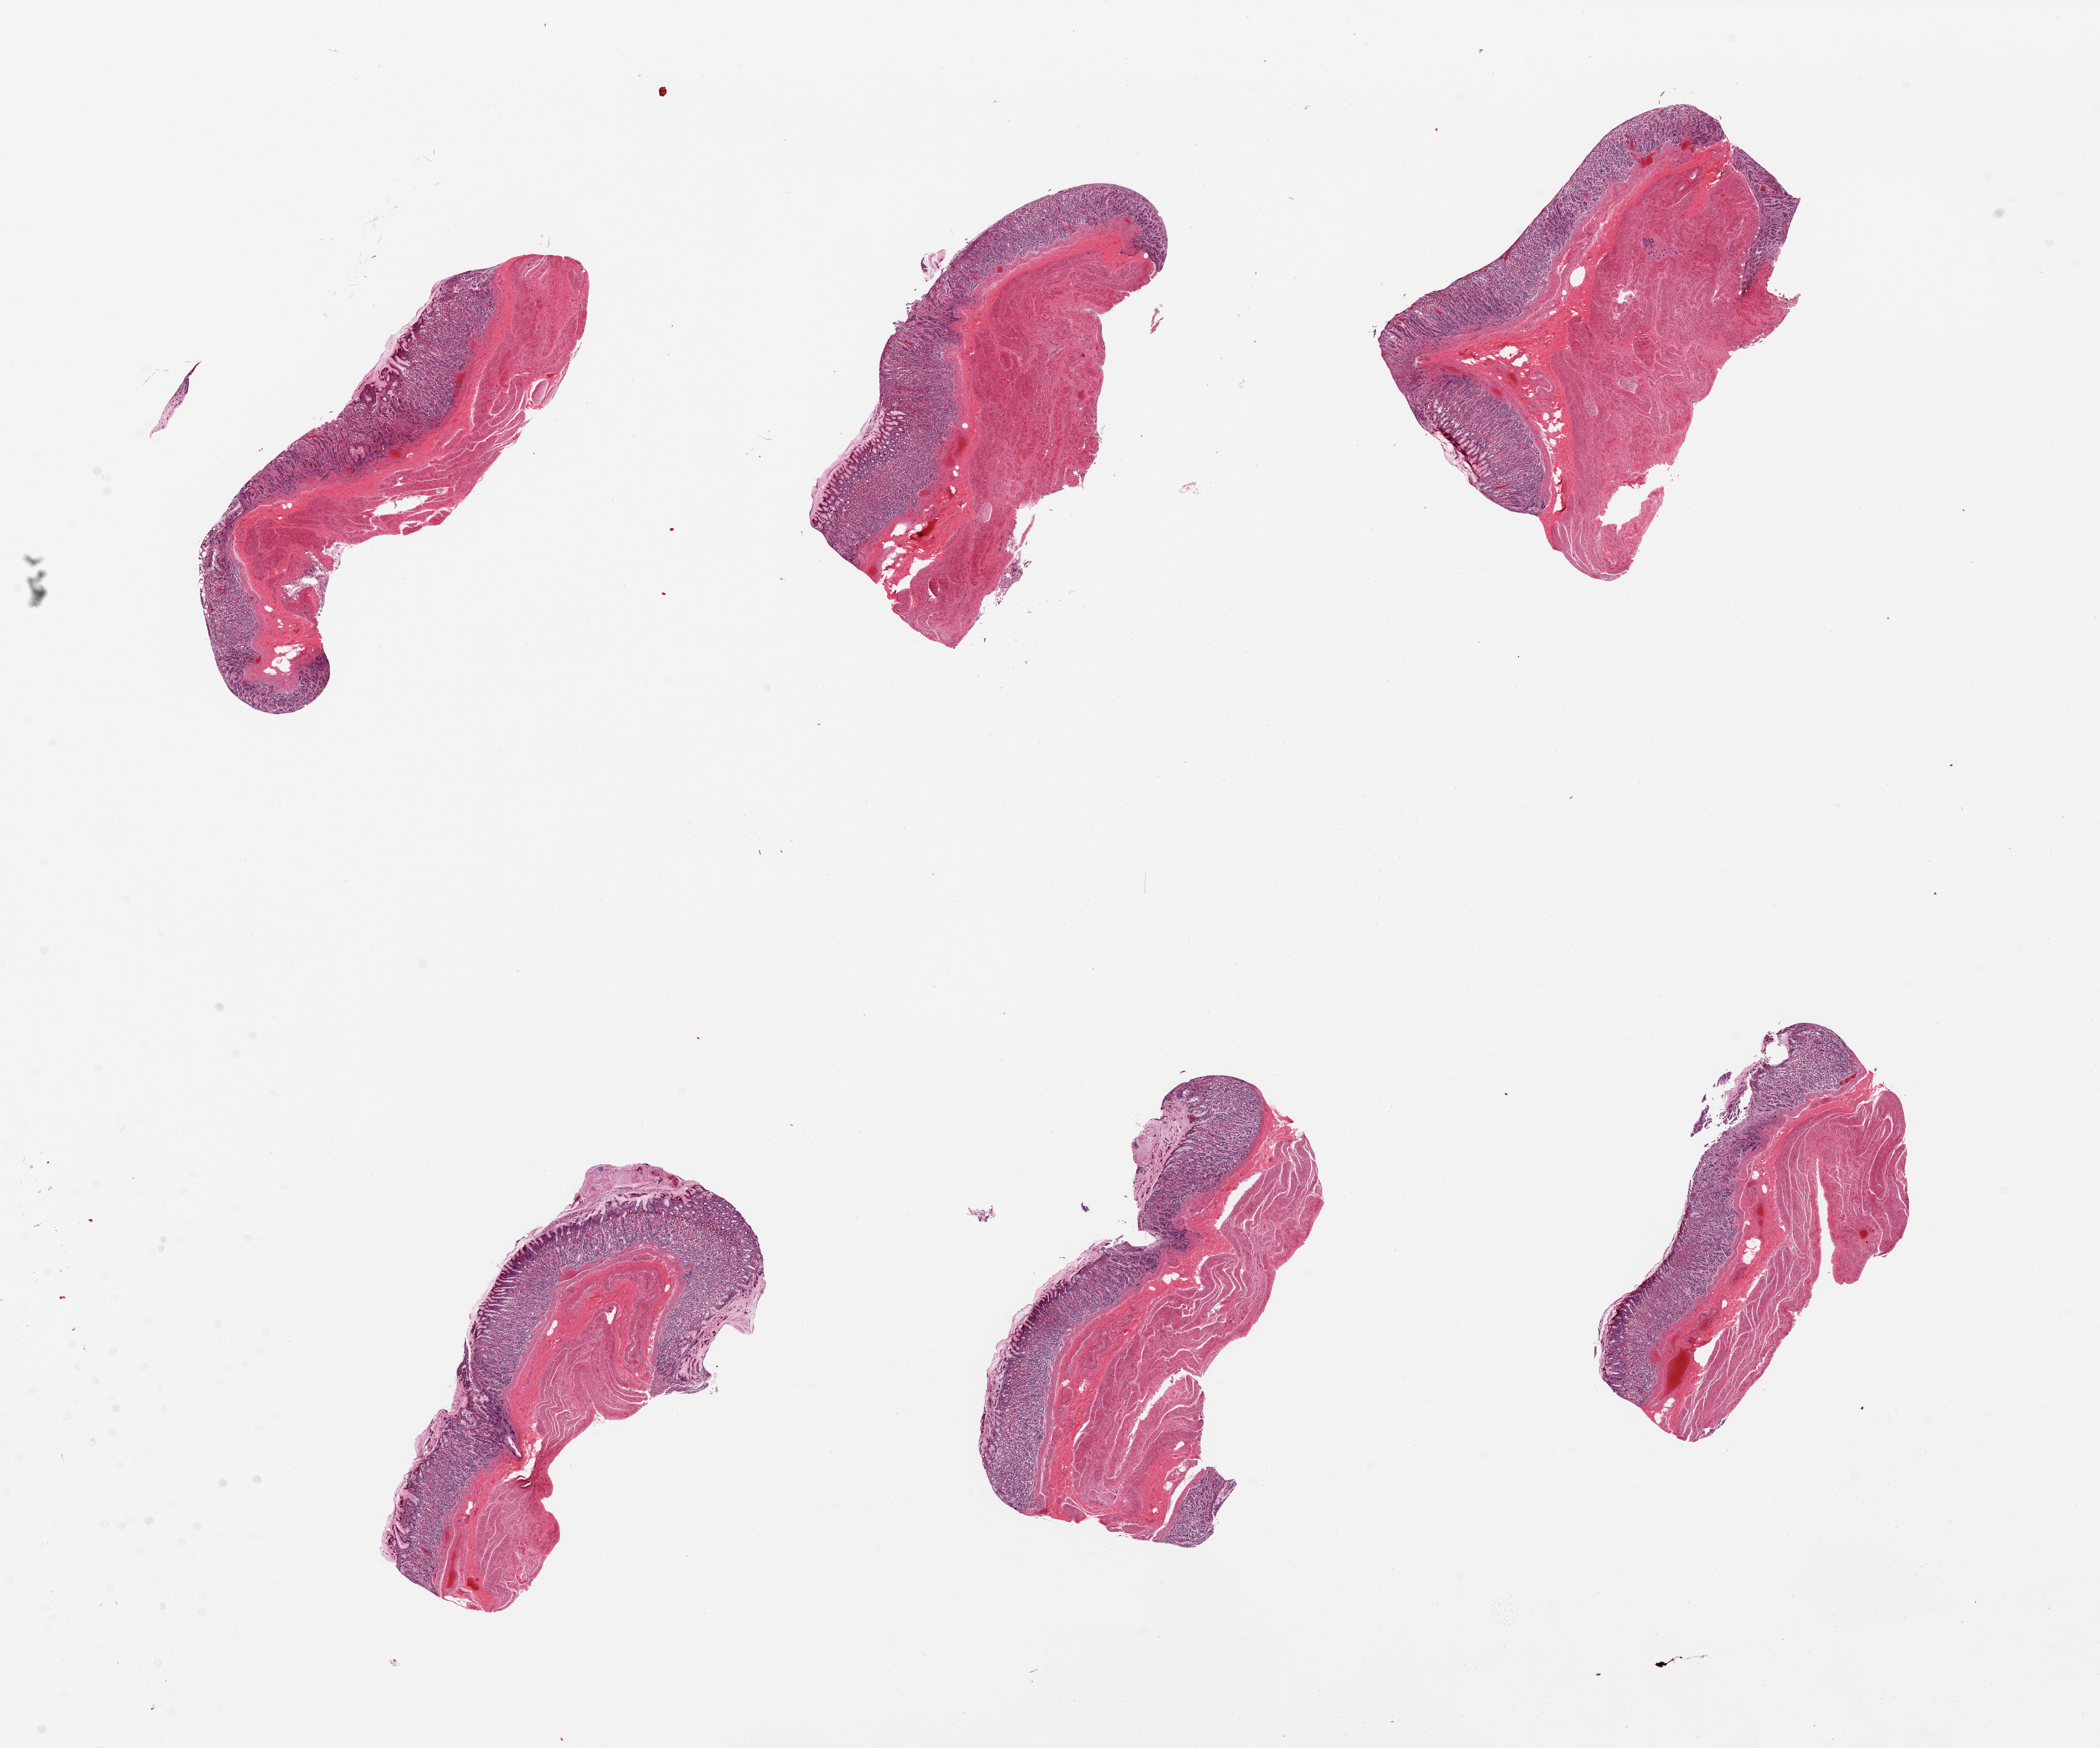
Haematoxylin and eosin whole-slide image, low-resolution overview of the scanned area, about 25.6 x 21.3 mm (slide scanned at 20x), PAXgene-fixed paraffin-embedded (PFPE) section, sampled site (target tissue): stomach, donor tissue sample. Donor sex: female.
• pathologist's review note for this sample: 6 pieces, mucosa is ~15-20% thickness but moderately to focally markedly autolyzed